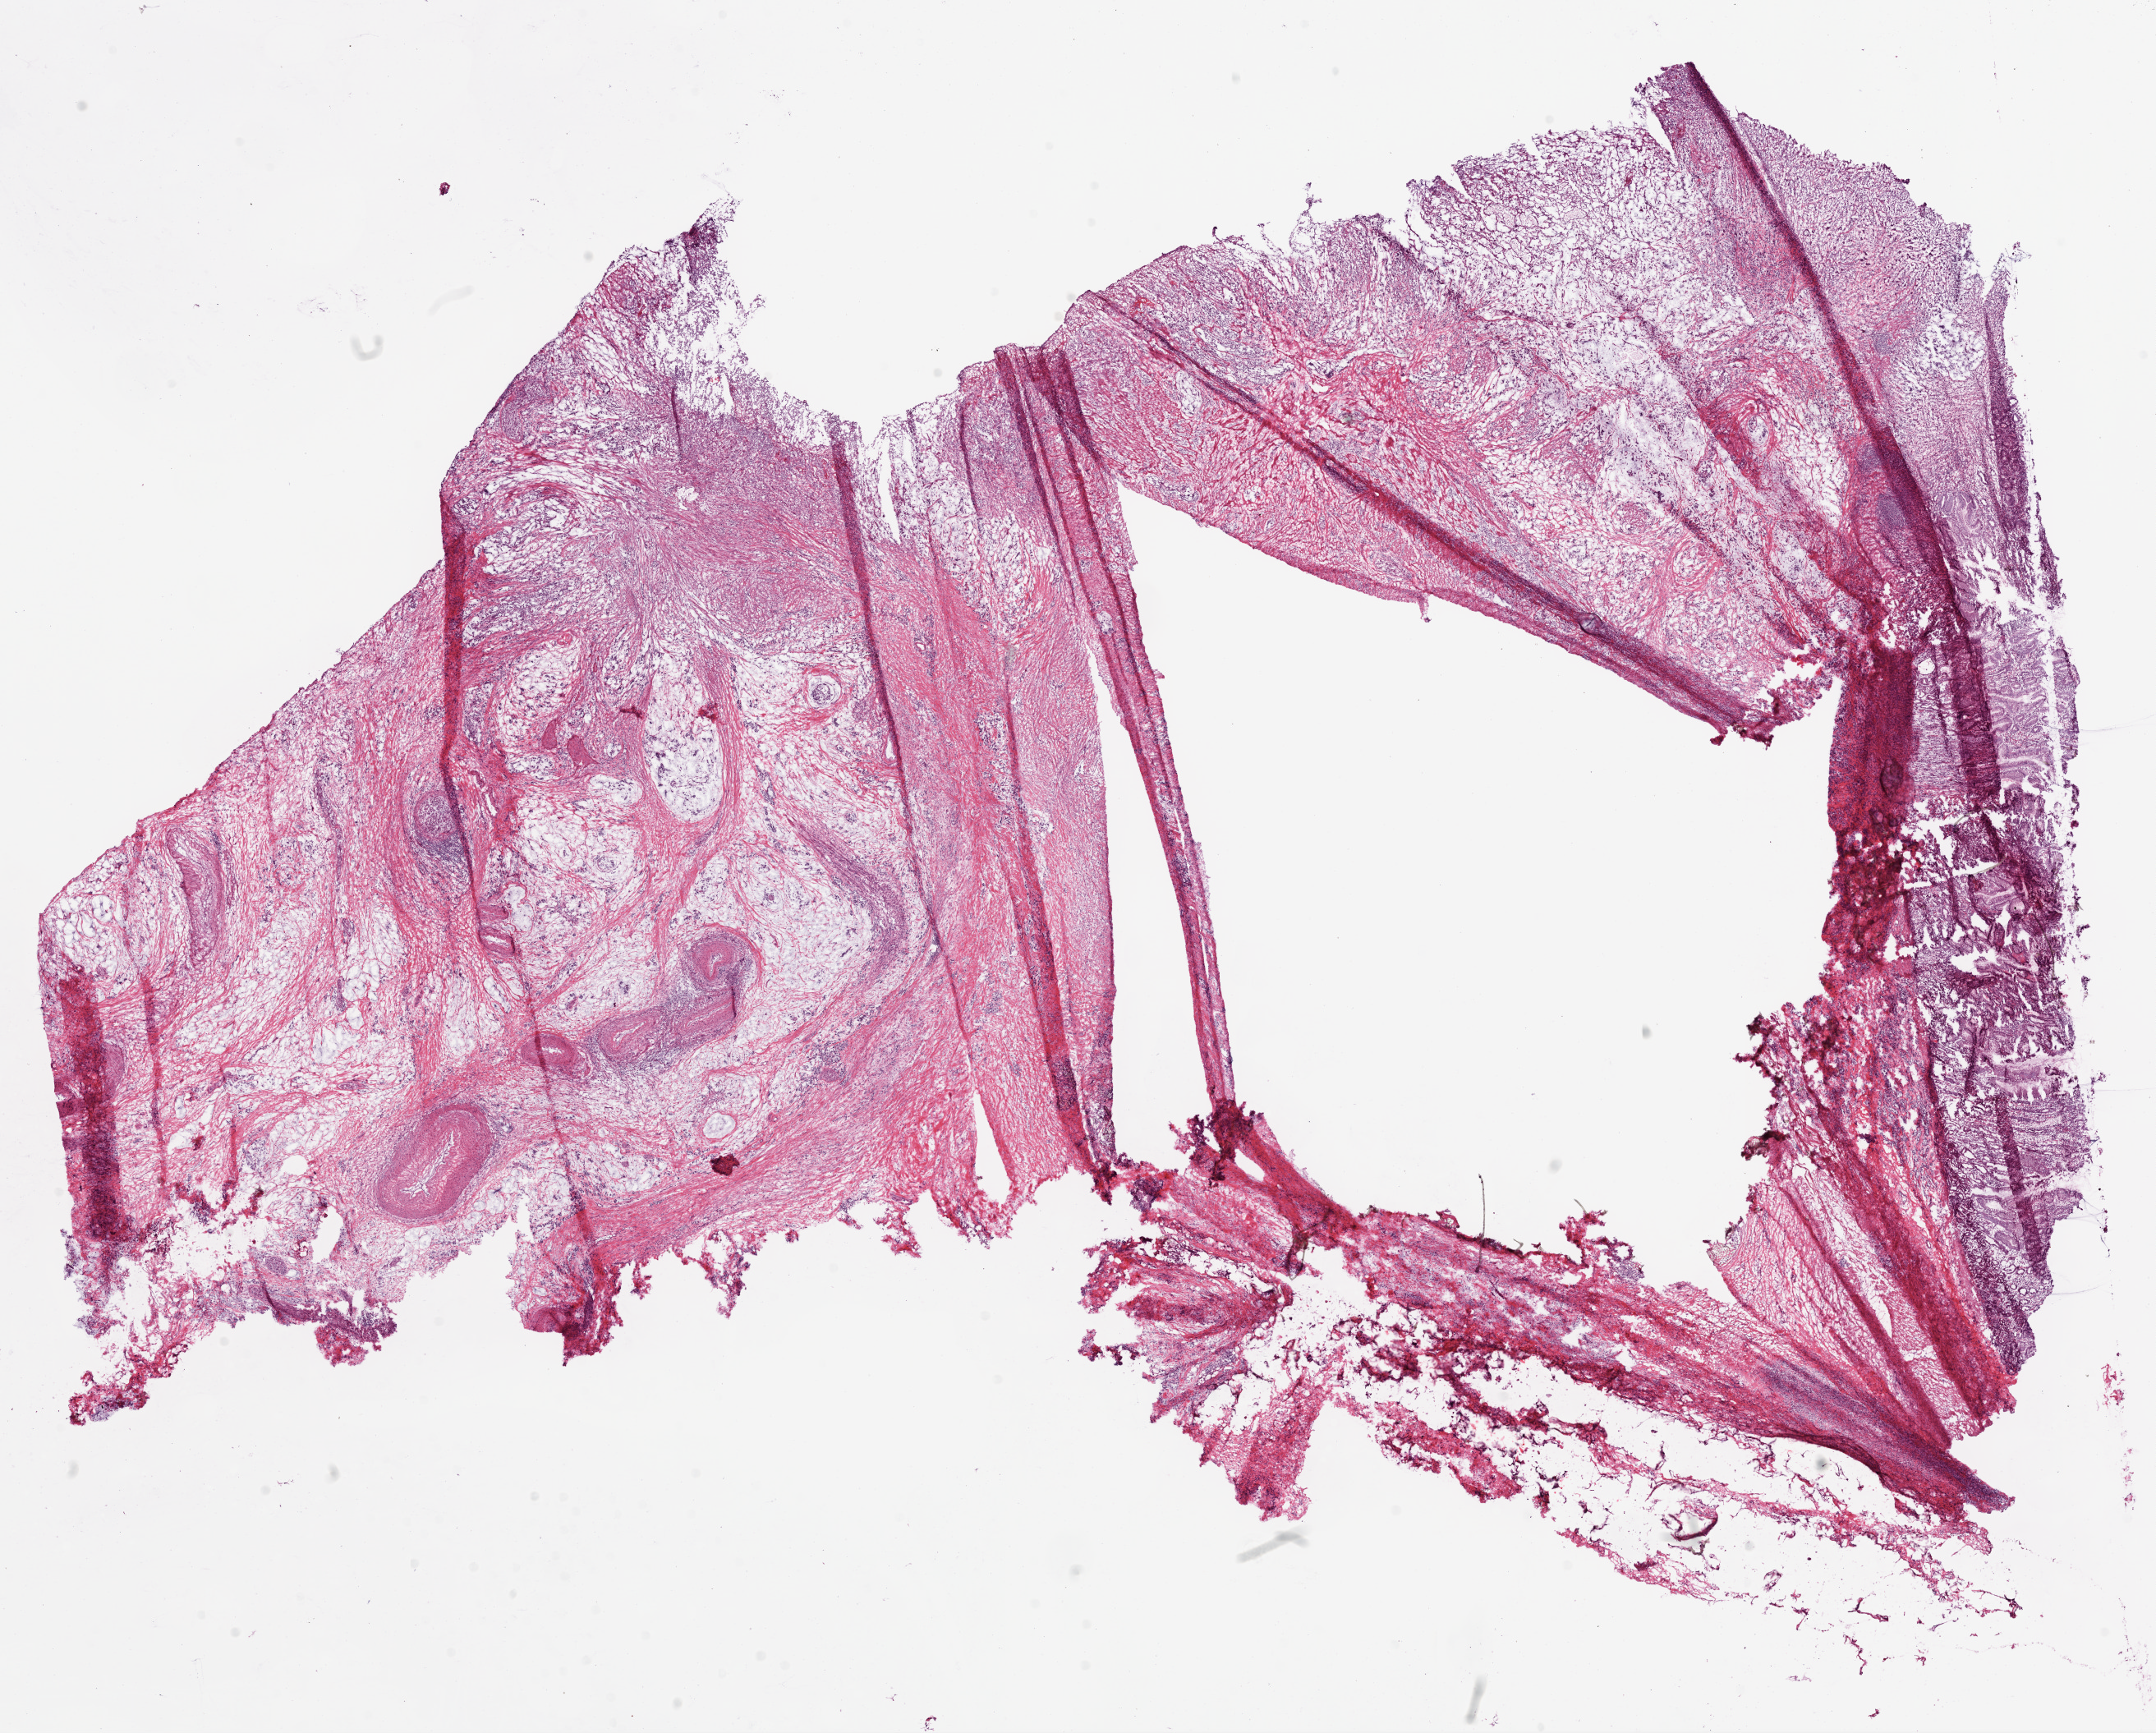
Digitized H&E-stained tissue section (whole slide), whole scanned area (about 21.1 x 16.9 mm, slide scanned at 20x) shown as a low-resolution overview; frozen section; stomach, primary tumour sample. Male, age 43 years at initial diagnosis. Histologic grade: G3 (poorly differentiated). Slide review estimates, as recorded: tumour cells 55%, tumour nuclei 75%, normal cells 5%, stromal cells 40%, necrosis 0%.
• diagnosis: Adenocarcinoma, NOS
• AJCC pathologic stage: II (6th edition)